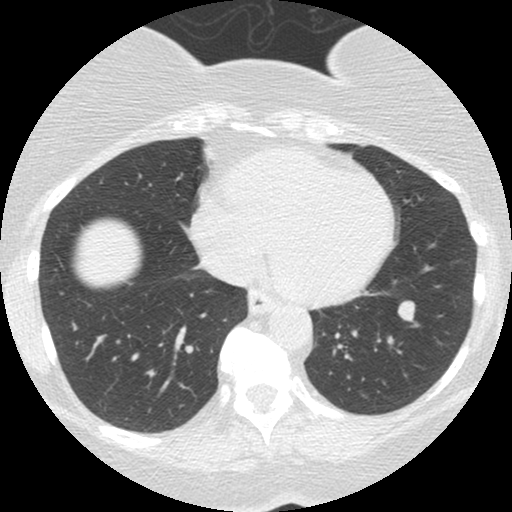
Low-dose screening chest CT, one axial slice; position 57 of 167 along the scan axis; 120 kVp; lung window (W 1500 / L -600 HU); 2.5 mm slice thickness; 512 × 512 image matrix.
Structures marked on this image (manually delineated by an expert):
- lesion 1 (tumor, lower lobe of left lung): bounding box (x1, y1, x2, y2) in pixels: (398, 301, 415, 321)